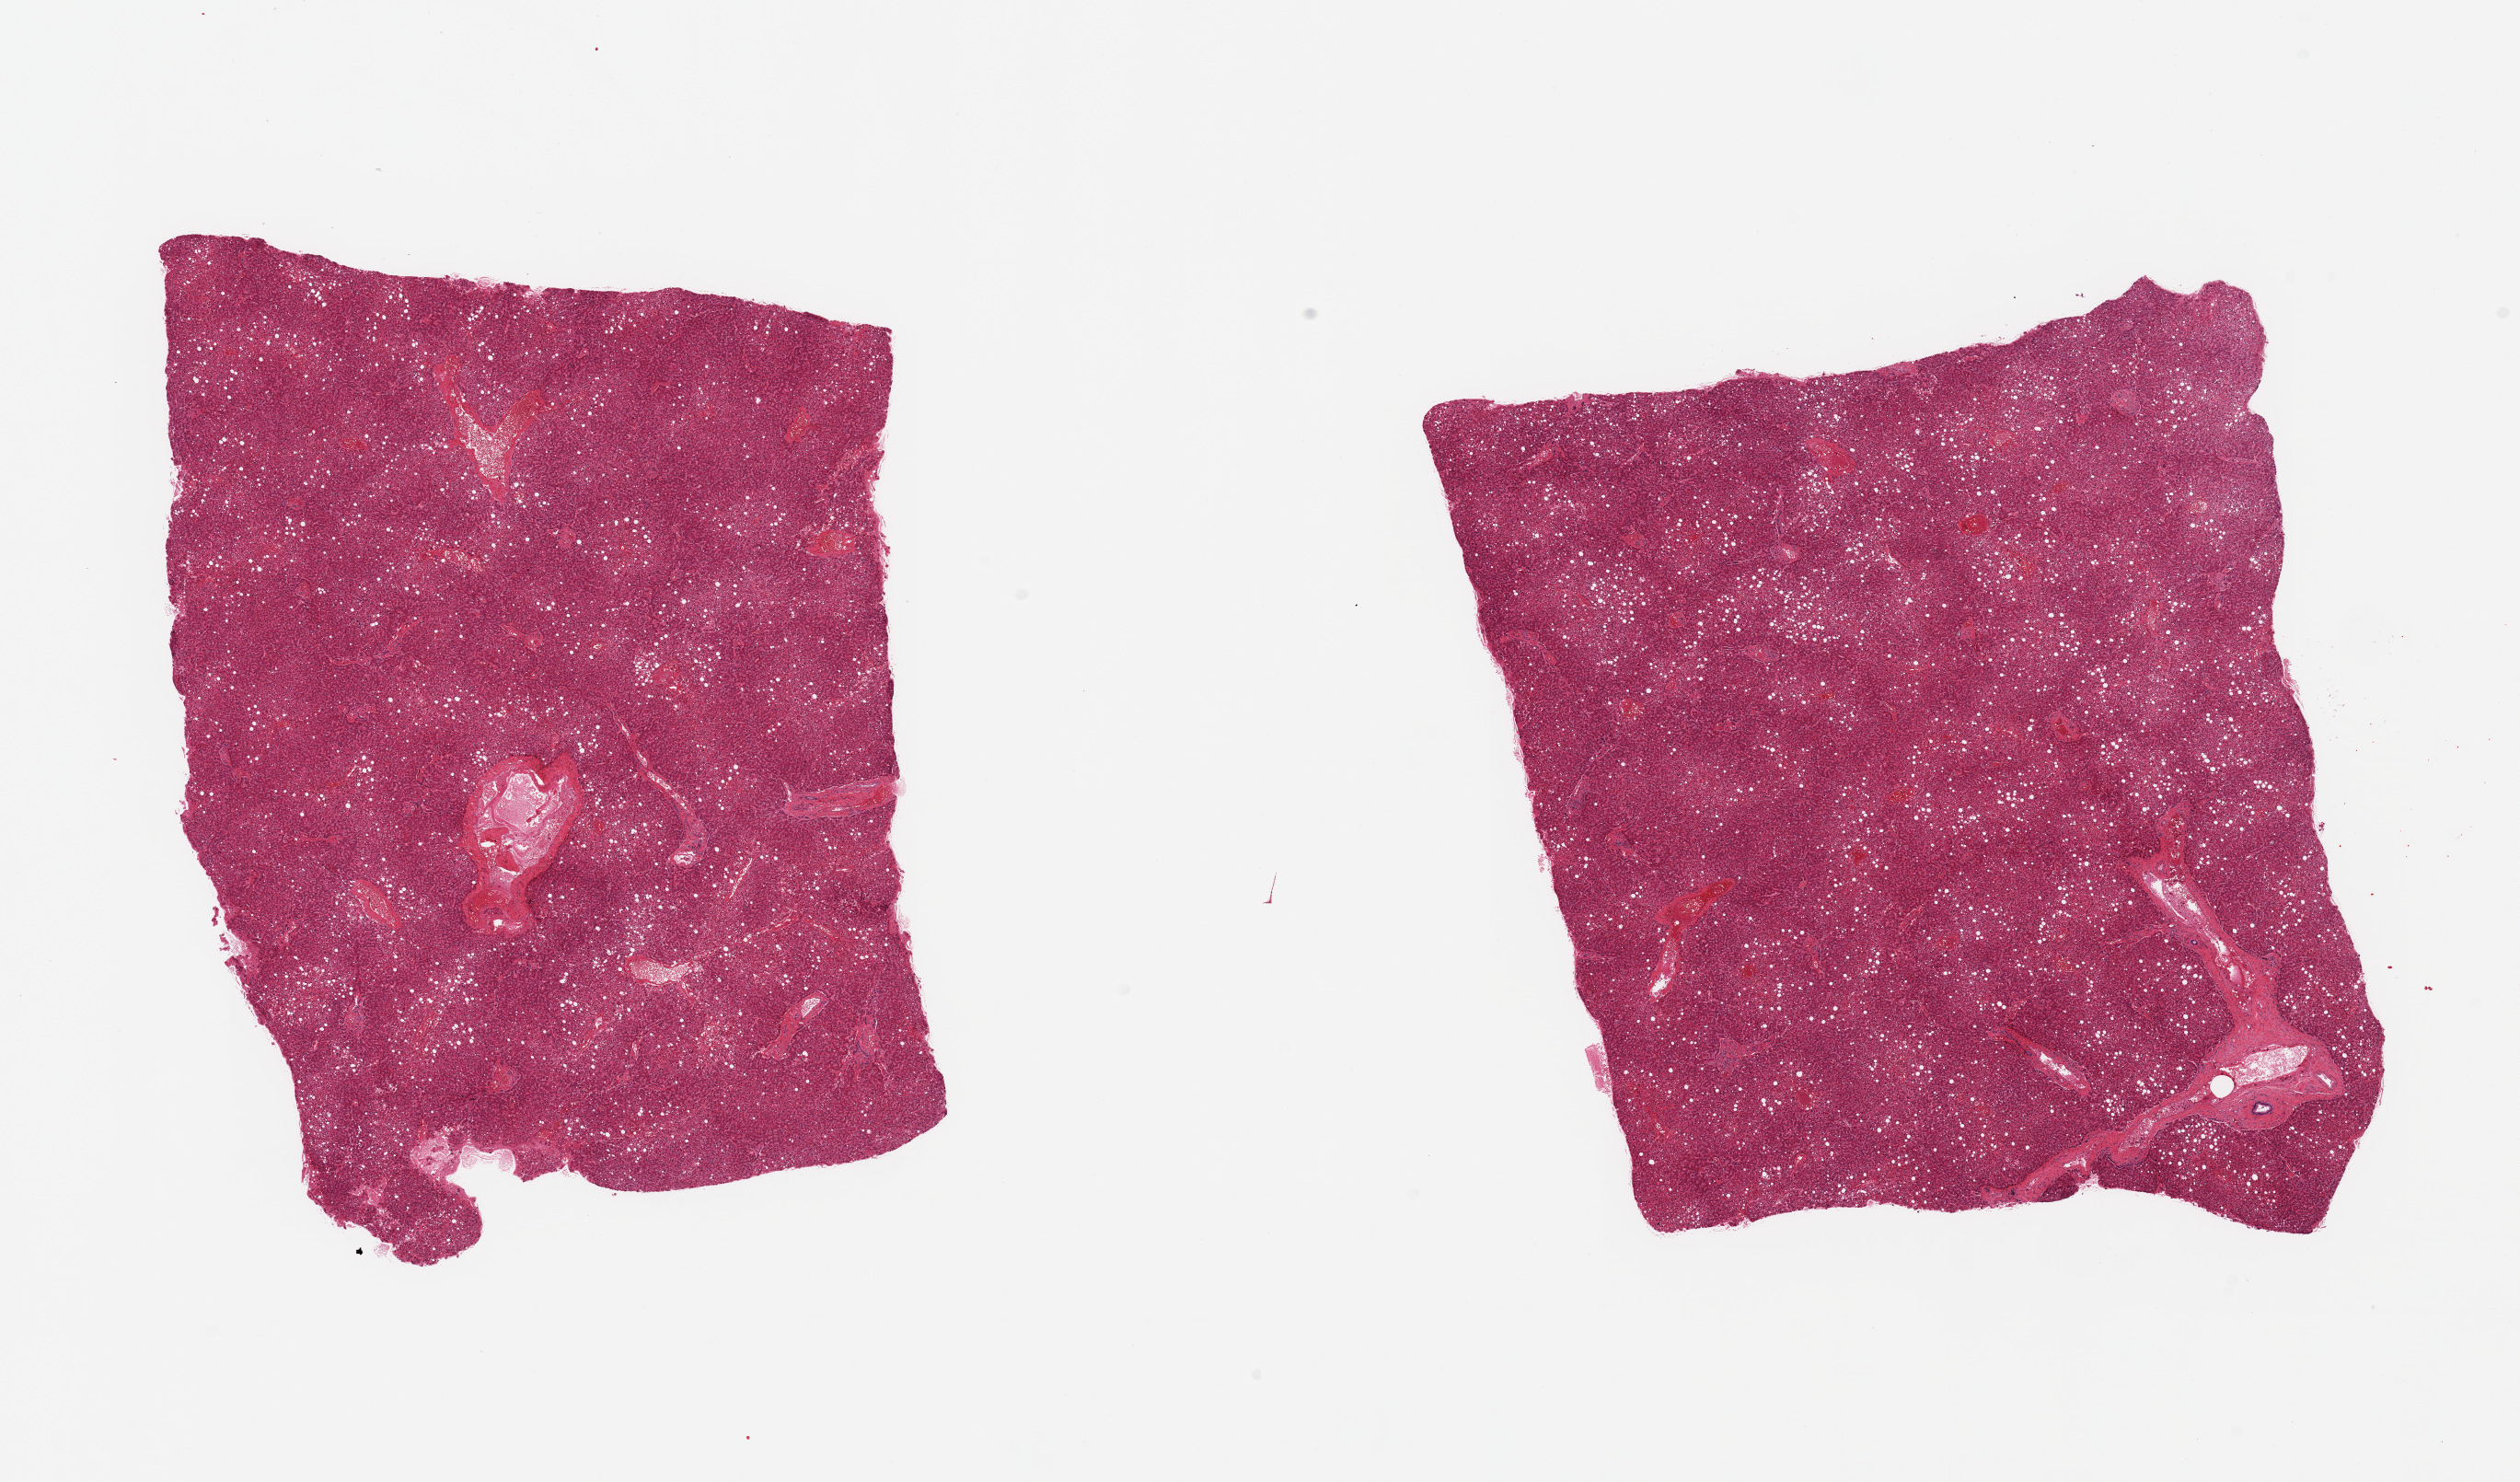
Digitized H&E-stained section, a low-resolution overview of the entire scanned area, about 21.7 x 12.7 mm (from a 20x scan). PAXgene-fixed, paraffin-embedded tissue. Sampled site (target tissue): liver. Tissue donor sample. Donor: female.
• reviewer comment on this tissue sample: 2 pieces; moderate [40%] macrovesicular steatosis mainly in central zones